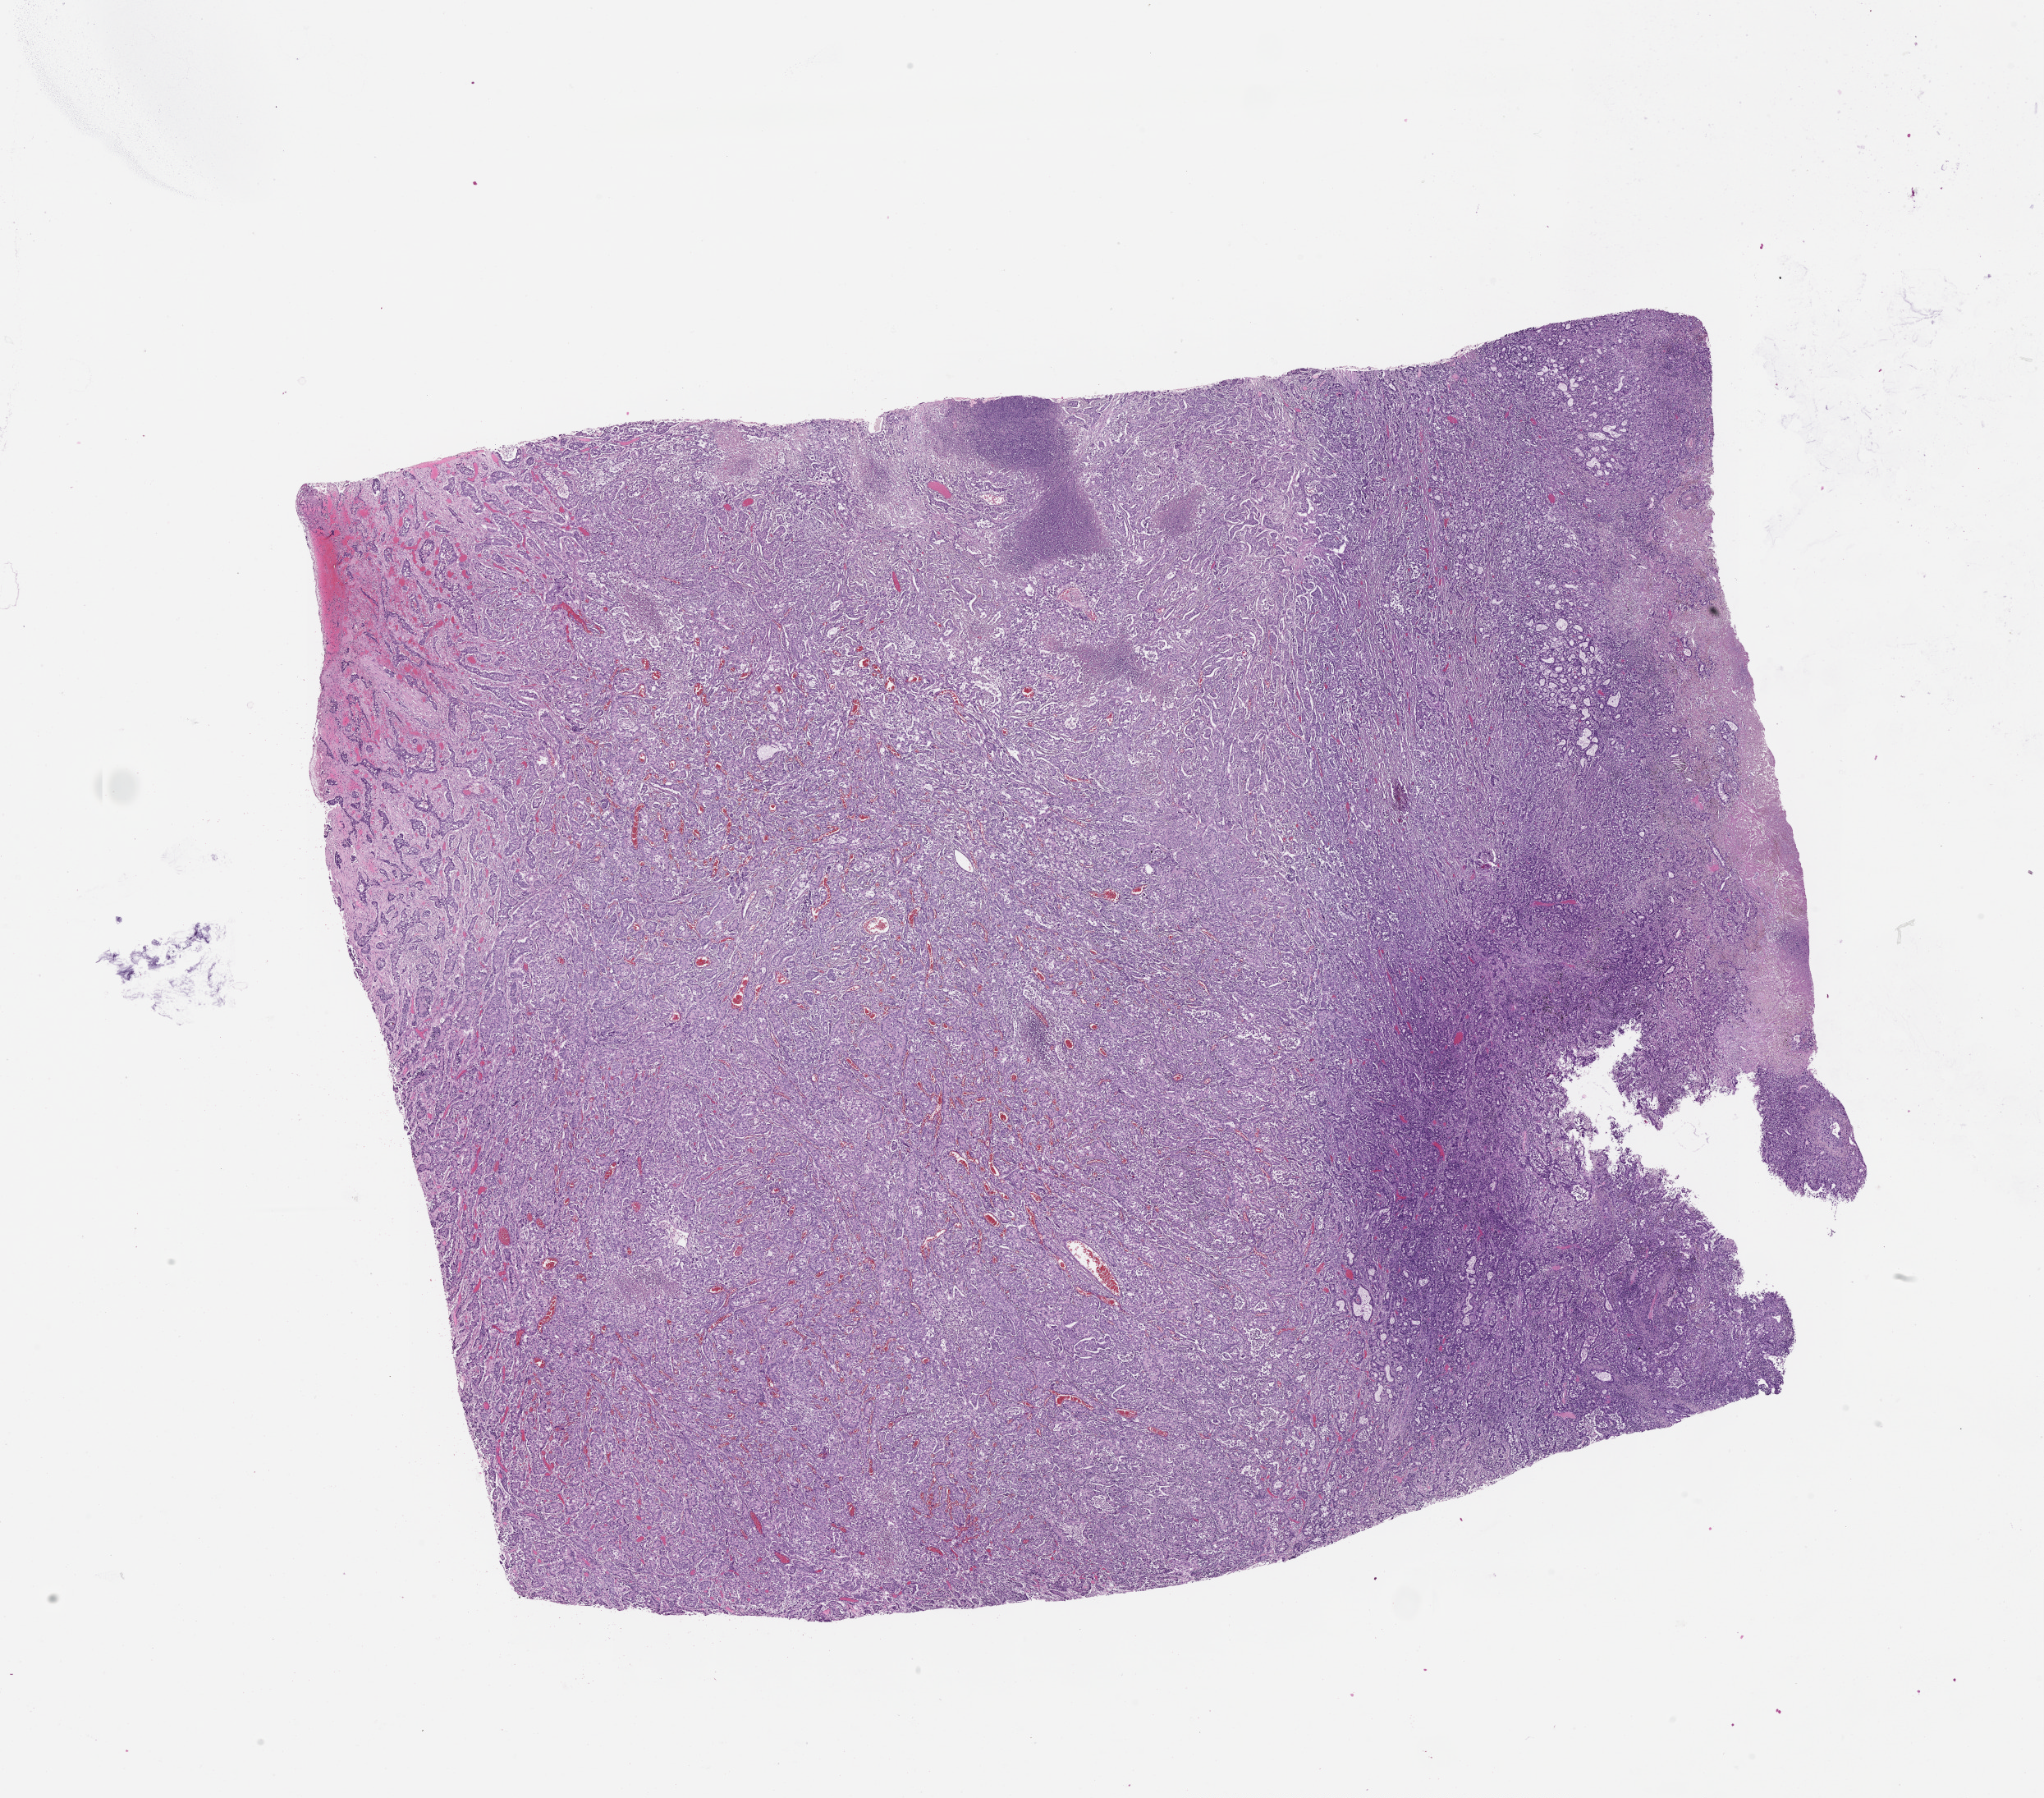
Whole-slide histology image, H&E-stained, a low-resolution overview of the entire scanned area, about 20.0 x 17.6 mm (acquisition: 20x scan), lung, tissue type not recorded.
Patient diagnosis (cohort enrolment): squamous cell carcinoma (lung).